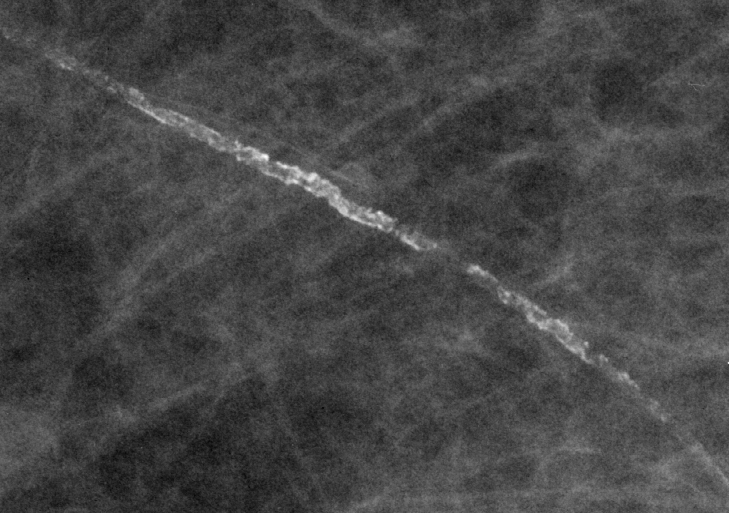
Cropped region of a digitized screen-film mammogram centred on a radiologist-marked abnormality; right breast; CC view; BI-RADS breast density category 2 (scale 1–4).
Calcifications, morphology vascular; BI-RADS assessment category 2; subtlety rating 5 on a 1 (subtle) to 5 (obvious) scale; benign without callback (not worked up further).